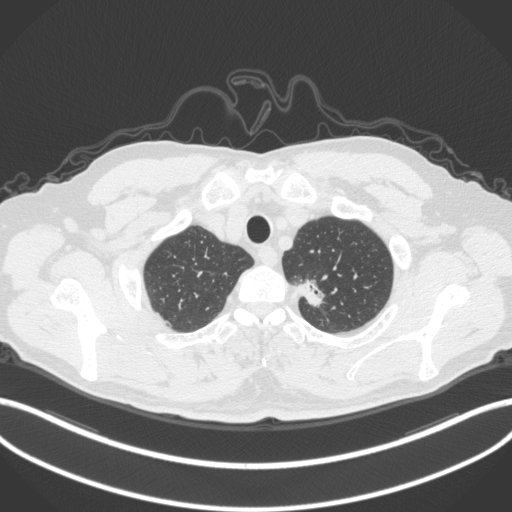
Chest CT, one axial slice. Position 337 of 382 along the scan axis. Reconstruction kernel B31f. Lung window (W 1500 / L -600 HU). 512 × 512 image matrix, field of view 400 × 400 mm. Patient: male, 64 years. From the clinical record (not read from this slice): clinical TNM (as recorded): T1c N0 M0.
Annotated regions visible in this slice (rectangle marked by the reading radiologist):
- lung tumour (recorded histology: adenocarcinoma): bounding box <295,272,336,313> (left, top, right, bottom; pixels)